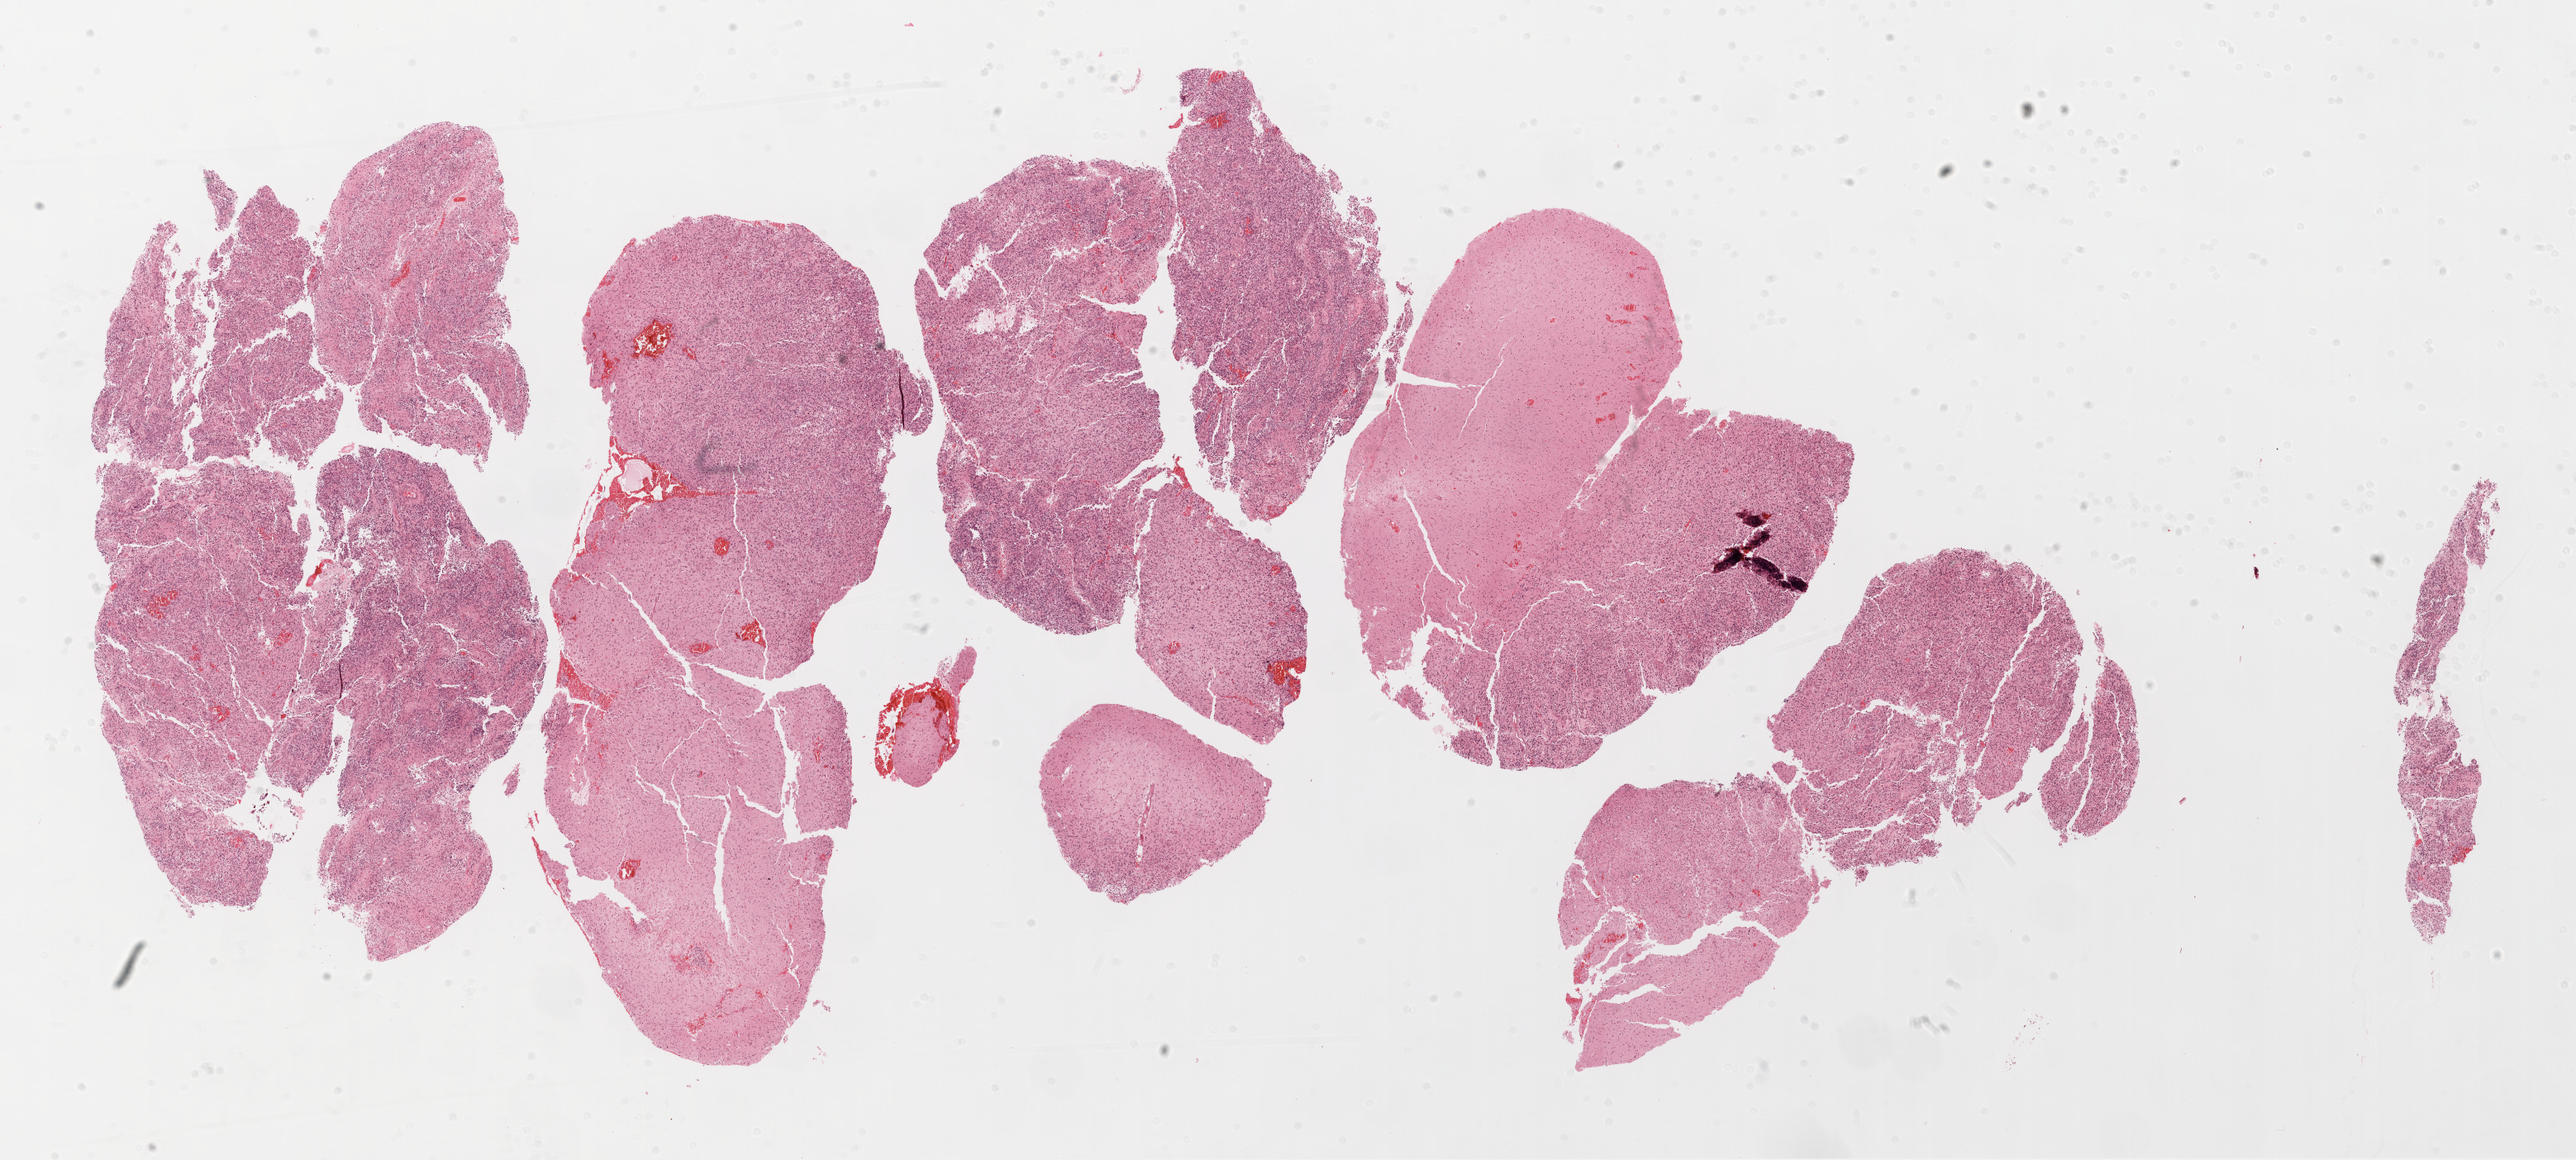
Whole-slide histology image, H&E, a low-resolution overview of the entire scanned area, about 25.1 x 11.3 mm. Formalin-fixed paraffin-embedded (FFPE) diagnostic section. Primary tumour sample from the brain. Patient: male, age at initial diagnosis 77 years.
Diagnosis: Glioblastoma.